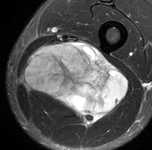
MRI of an extremity soft-tissue mass, one axial slice; slice 46 of 90 in the series (ordered by position); STIR; MR volume resampled by the dataset authors to the PET/CT grid (not the native acquisition matrix); 3.27 mm slice thickness; 152 × 150 image matrix. Male patient. From the clinical record (not read from this slice): histological type: undifferentiated pleomorphic liposarcoma; grade: high; site of the primary tumour: left thigh.
Outlined on this slice (expert contour drawn on MRI and transferred to this co-registered scan by the dataset authors):
- gross tumour volume including surrounding oedema: box from (x=23, y=43) to (x=129, y=125) px
- gross tumour volume (mass): (x=25, y=43)–(x=129, y=125)